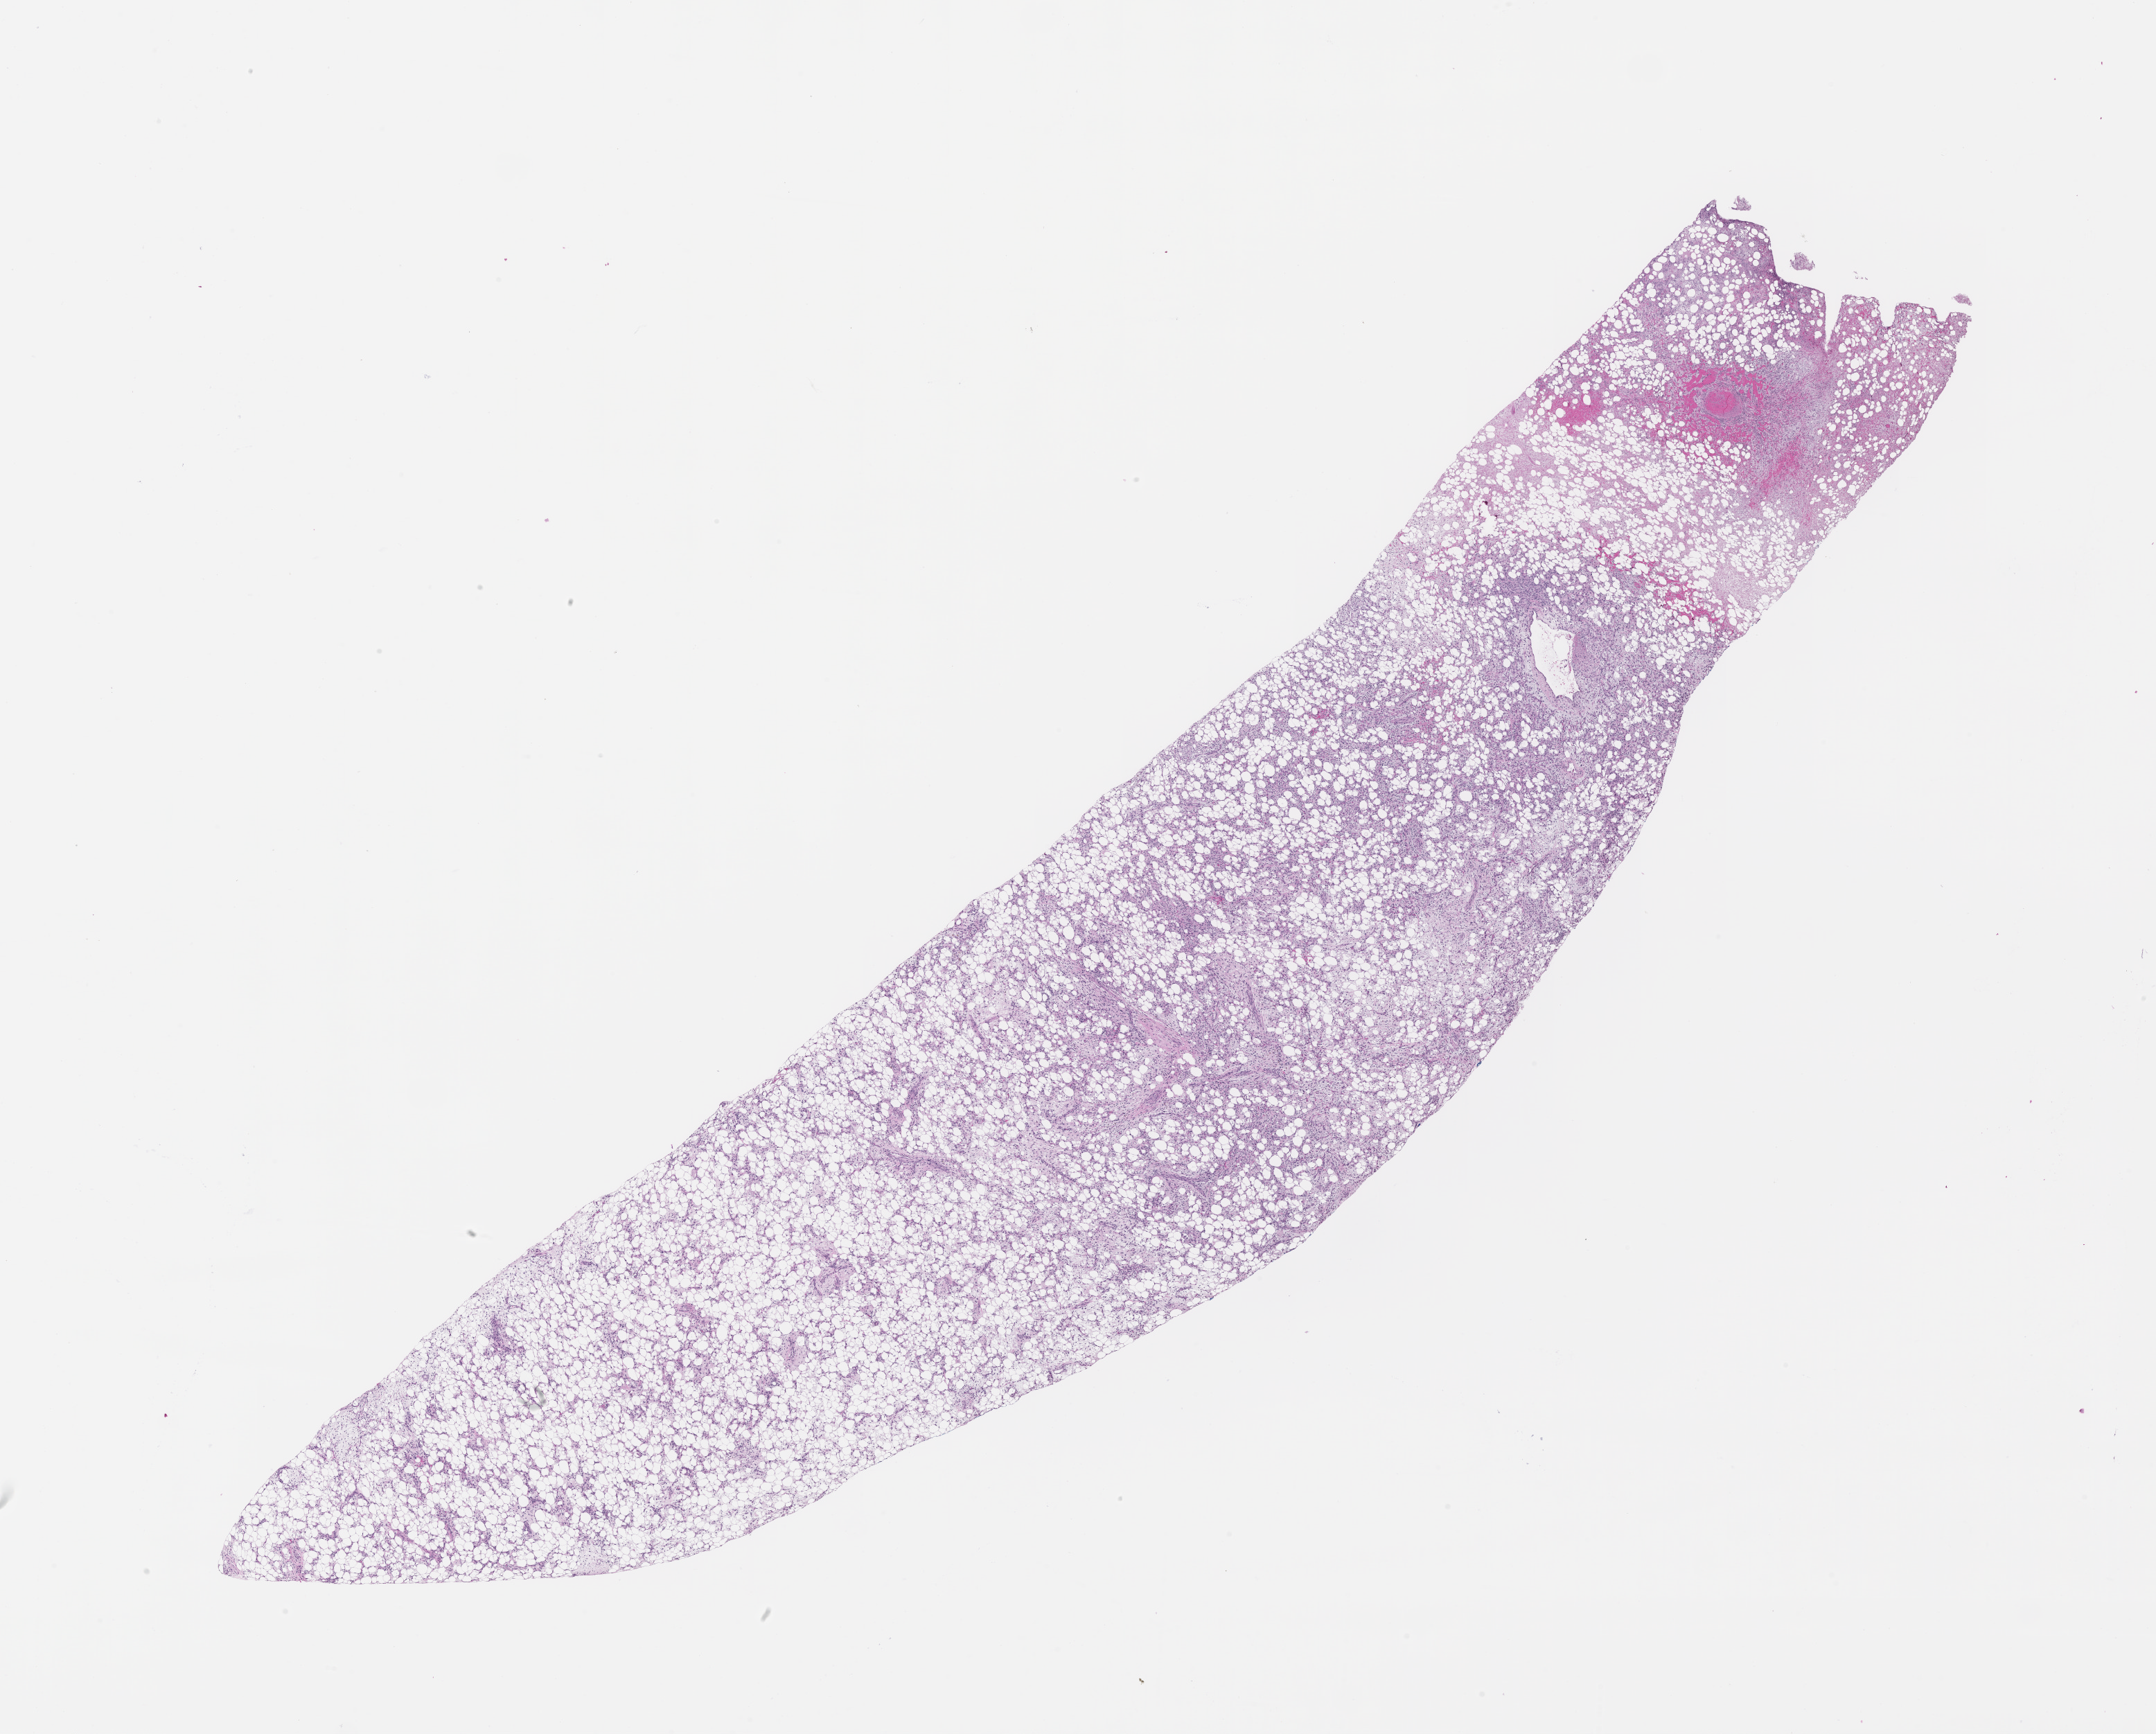
Digitized H&E-stained tissue section (whole slide) — whole scanned area (about 25.1 x 20.2 mm) shown as a low-resolution overview.
Patient diagnosis (cohort enrolment): sarcoma (site not recorded at cohort level).